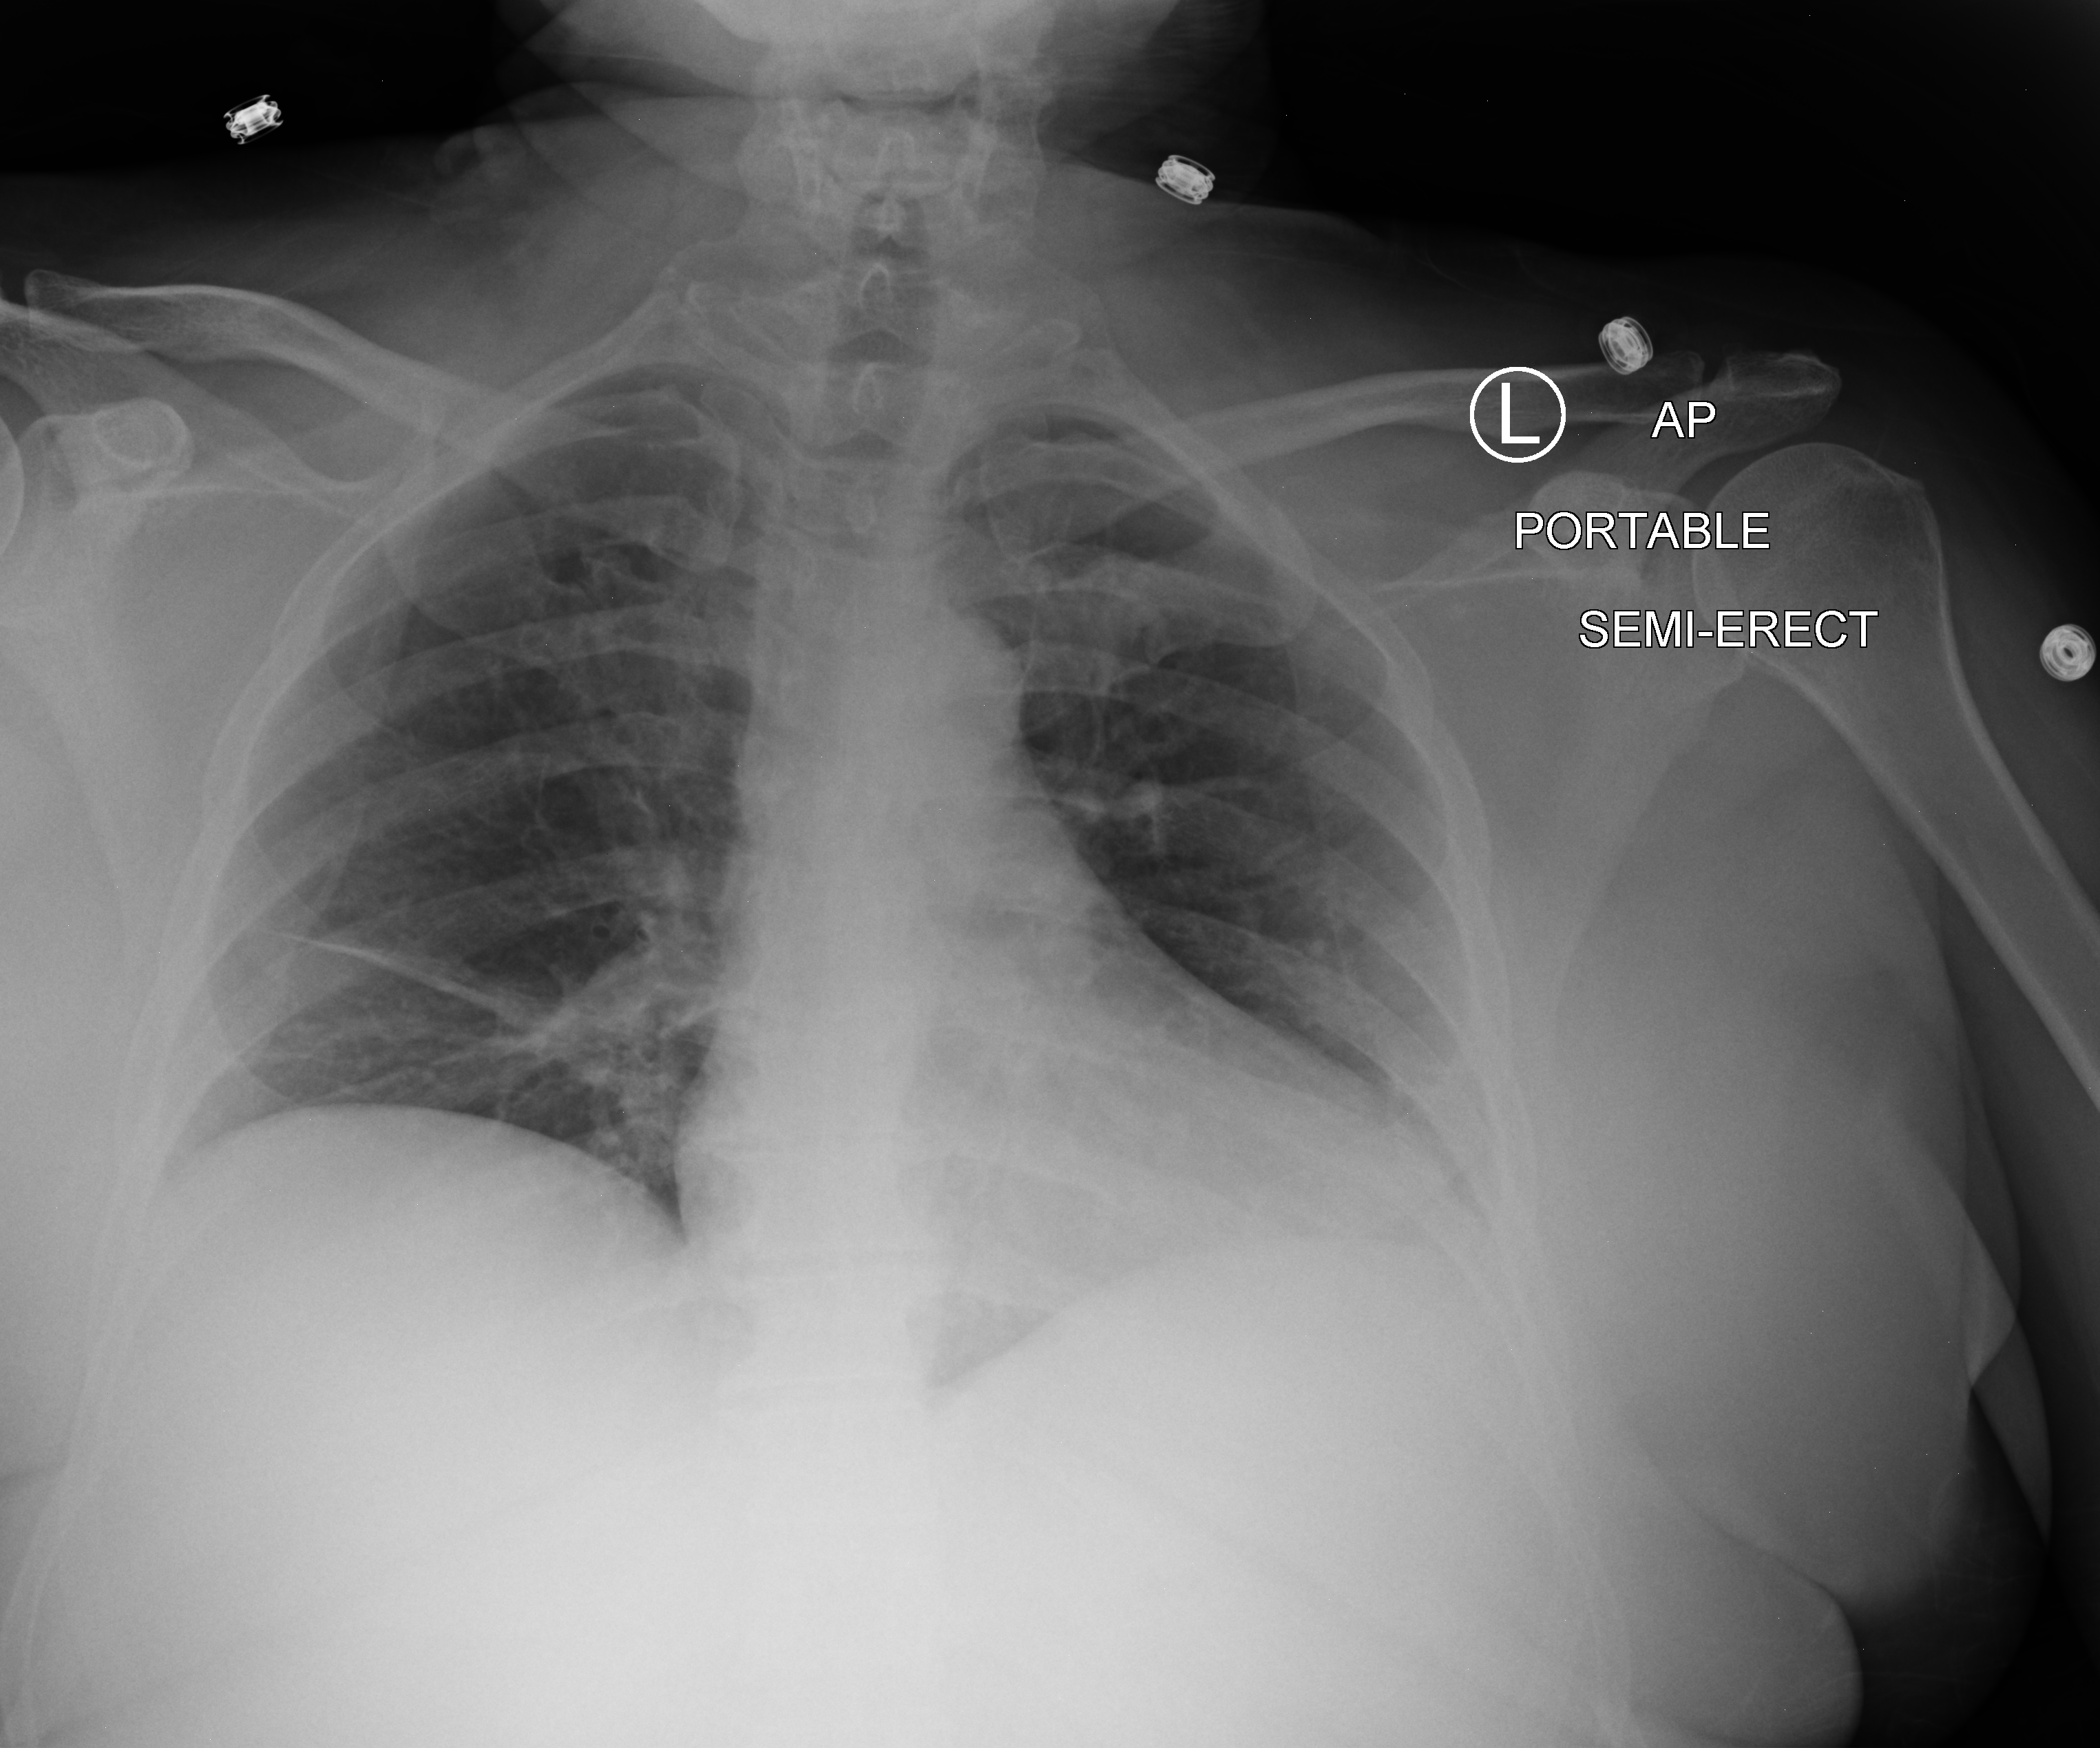
Portable chest radiograph. Female patient hospitalised with COVID-19, age 60–74 years.
Hospital-stay facts (about this admission, not read from this image; timing relative to this image not recorded): length of hospital stay: 50 days; admitted to intensive care during this hospital stay: yes.